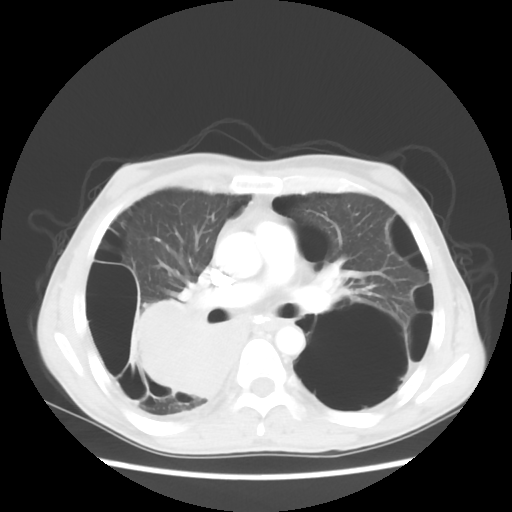
Chest CT, one axial slice; slice 31 of 56 in the series (ordered by position); reconstruction kernel STANDARD; lung window (W 1500 / L -600 HU); 5 mm slice thickness; 512 × 512 image matrix, field of view 351 × 351 mm. Male patient, age 41 years. From the clinical record (not read from this slice): clinical TNM (as recorded): T4 N0 M1a; histopathological grade: G3.
Structures marked on this image (rectangle marked by the reading radiologist):
- lung tumour (recorded histology: large cell carcinoma): bounding box <117,292,259,412> (left, top, right, bottom; pixels)